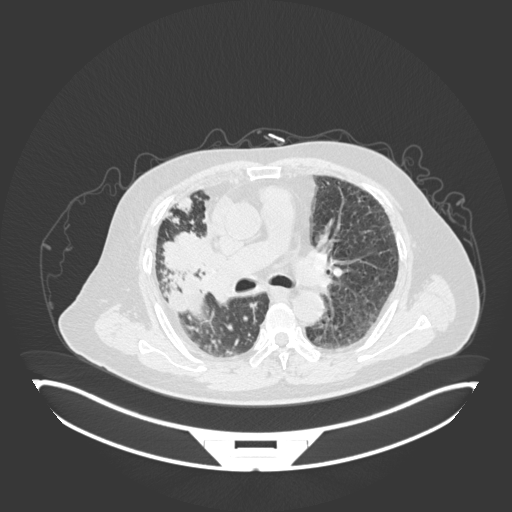
Chest CT, one axial slice. Position 99 of 201 along the scan axis. 120 kVp. Lung window (W 1500 / L -600 HU). 1 mm slice thickness. 512 × 512 image matrix, field of view 500 × 500 mm. Male patient, age 69 years. Case-level facts recorded for this patient, not image findings: clinical TNM (as recorded): T4 N3 M1.
Structures marked on this image (bounding box drawn by a radiologist):
- lung tumour (recorded histology: adenocarcinoma): bounding box <160,227,219,277> (left, top, right, bottom; pixels)